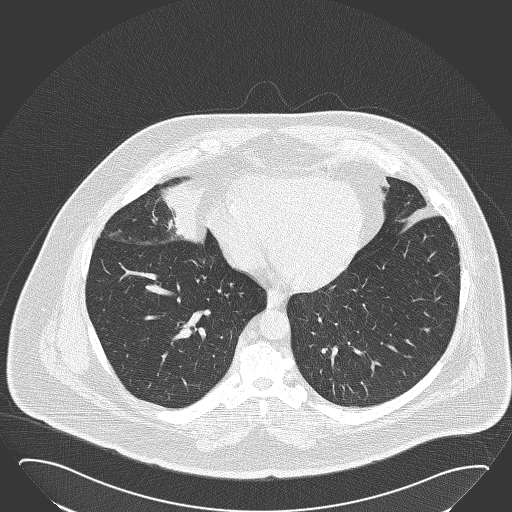
Low-dose screening chest CT, one axial slice. Slice 61 of 168 in the series (ordered by position). Reconstruction kernel B50f. 120 kVp. Lung window (W 1500 / L -600 HU). 2 mm slice thickness. 512 × 512 image matrix.
Annotated regions visible in this slice (expert manual segmentation):
- lesion 1 (tumor, hilum of right lung): bounding box [x1, y1, x2, y2] px = [161, 180, 203, 243]